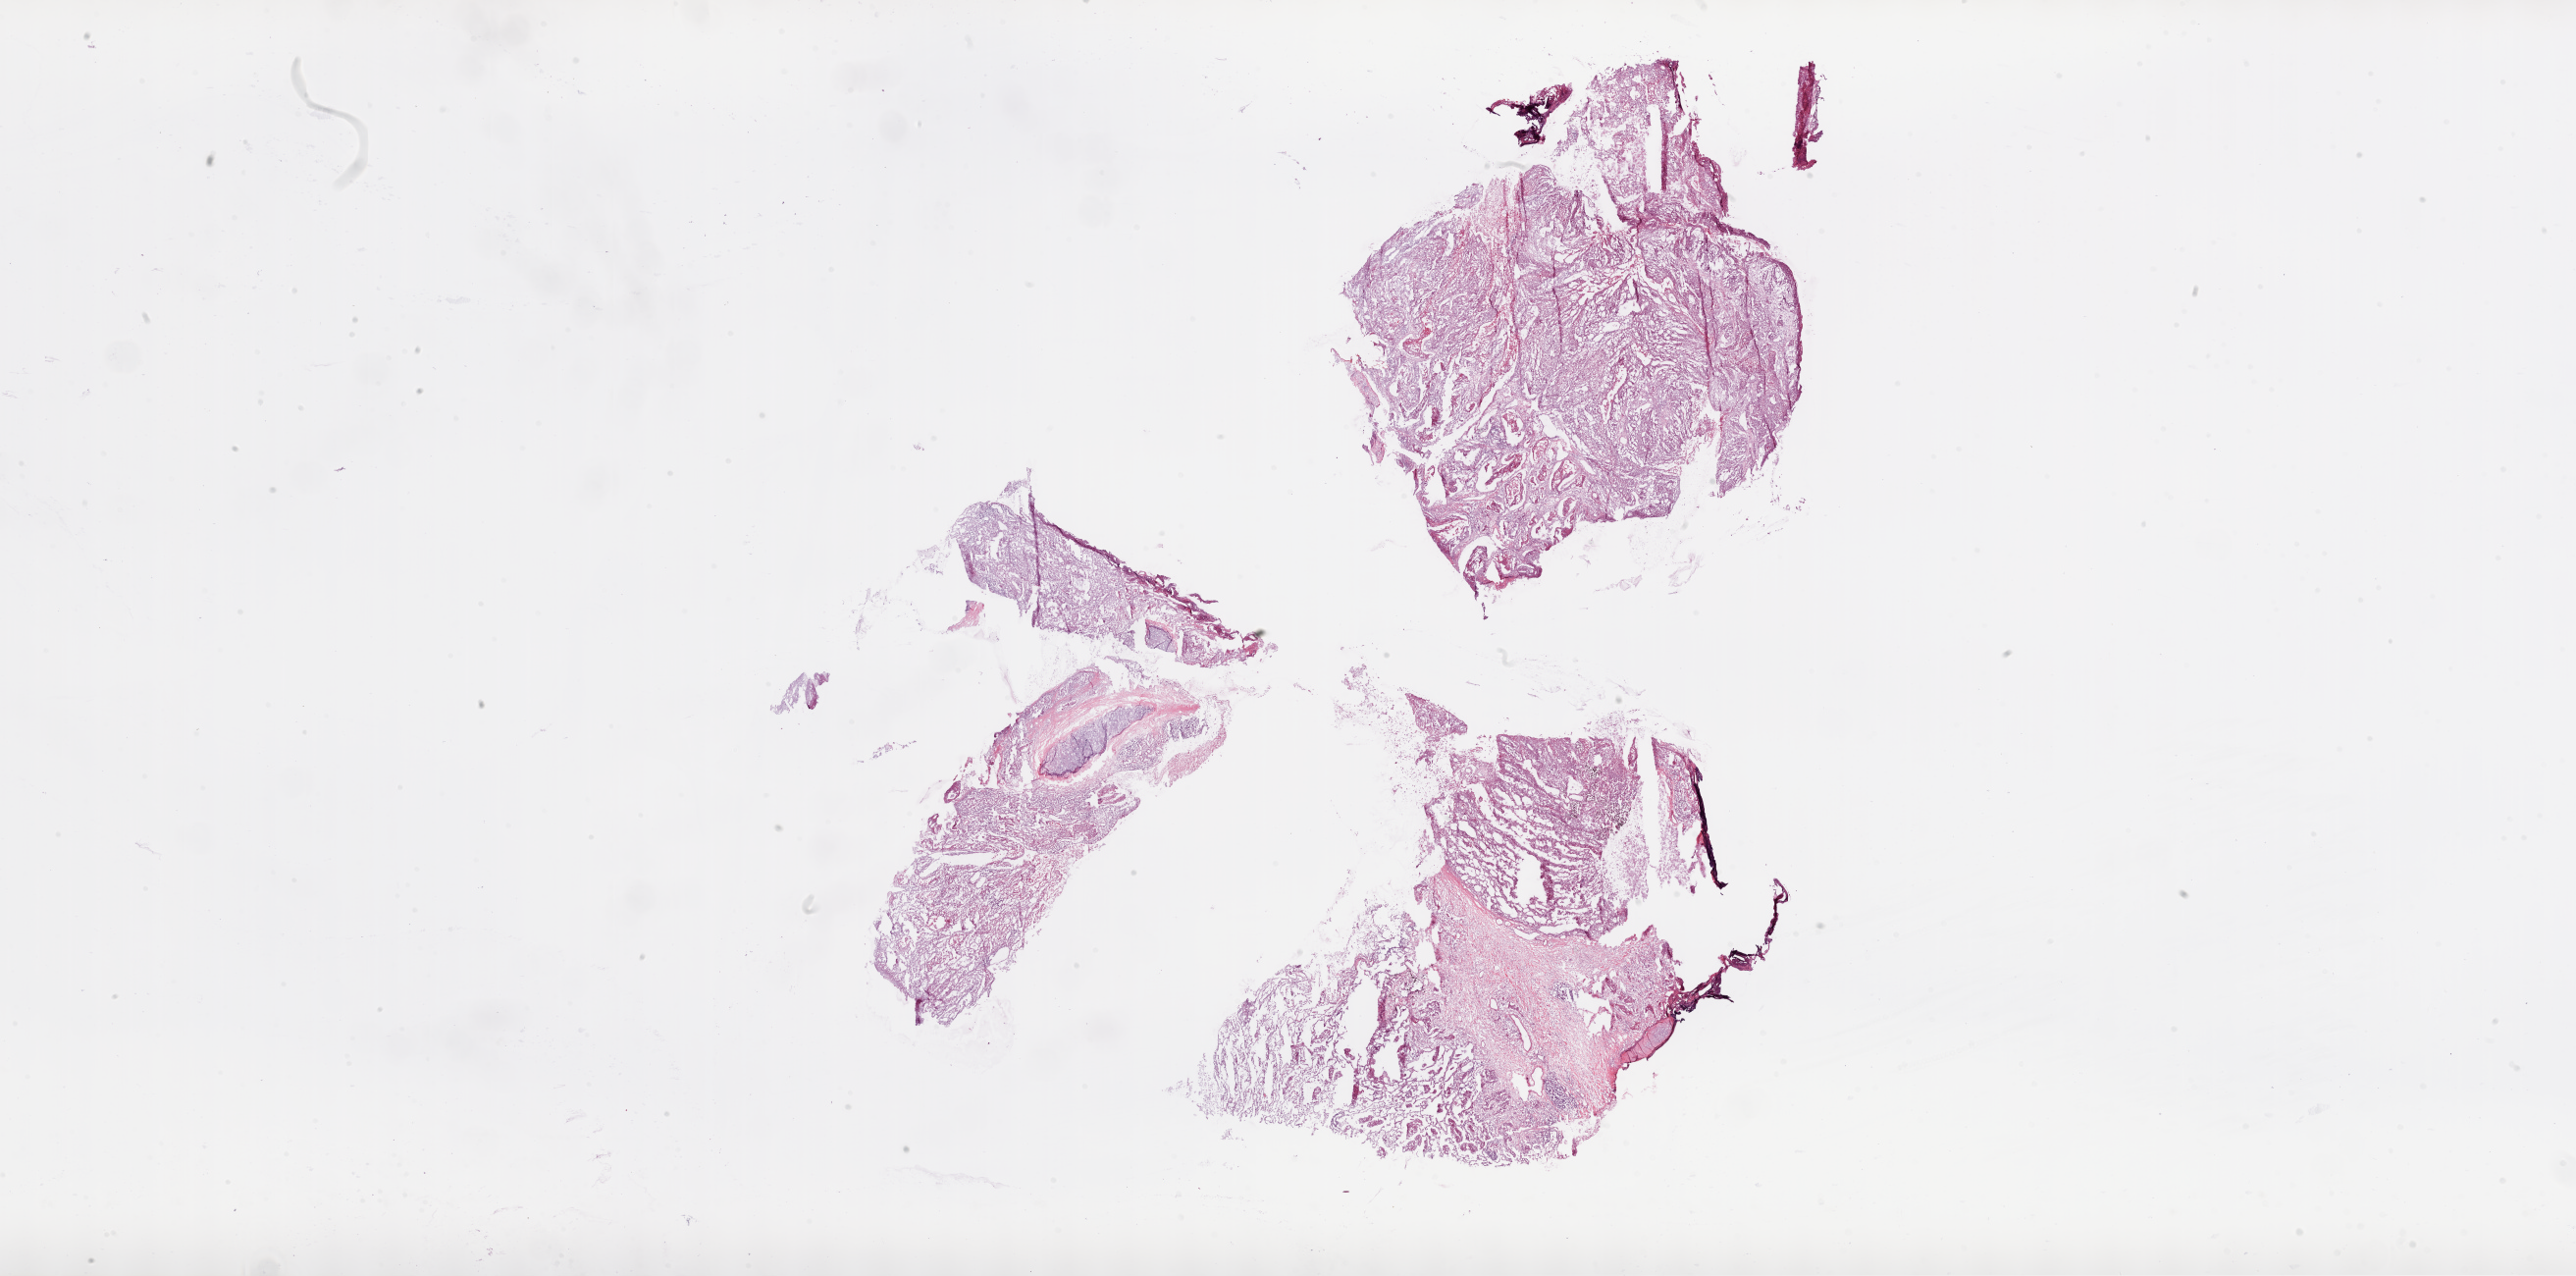
Whole-slide histology image, Hematoxylin and eosin (H&E) stained — a low-resolution overview of the entire scanned area, about 42.1 x 20.9 mm; frozen section from the bottom of the tissue portion; lung, primary tumour sample. Female, age 65 years at initial diagnosis. Slide review estimates, as recorded: tumour cells 68%, tumour nuclei 70%, normal cells 18%, stromal cells 9%, necrosis 5%. Inflammatory infiltration, as recorded: lymphocyte infiltration 15%, monocyte infiltration 2%, neutrophil infiltration 2%.
* AJCC pathologic stage: IIIA (7th edition)
* TNM: T2a N2 M0
* histologic diagnosis: Squamous cell carcinoma, NOS